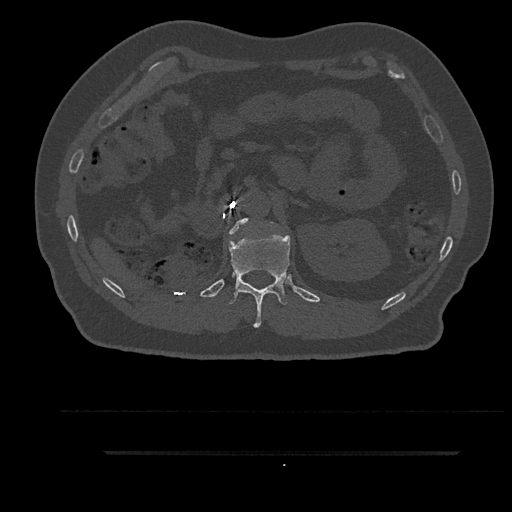
CT including the spine, one axial slice. Position 231 of 797 along the scan axis. Reconstruction kernel Br40s/3. 120 kVp. Bone window (W 1800 / L 400 HU). 512 × 512 image matrix, field of view 432 × 432 mm. Patient: male, 63 years. Case-level facts recorded for this patient, not image findings: primary cancer: renal.
Structures marked on this image (semi-automatic segmentation, software-assisted and operator-edited):
- L1 vertebra: bounding box [x1, y1, x2, y2] px = [229, 219, 248, 234]
- T12 vertebra: [228, 231, 290, 328]